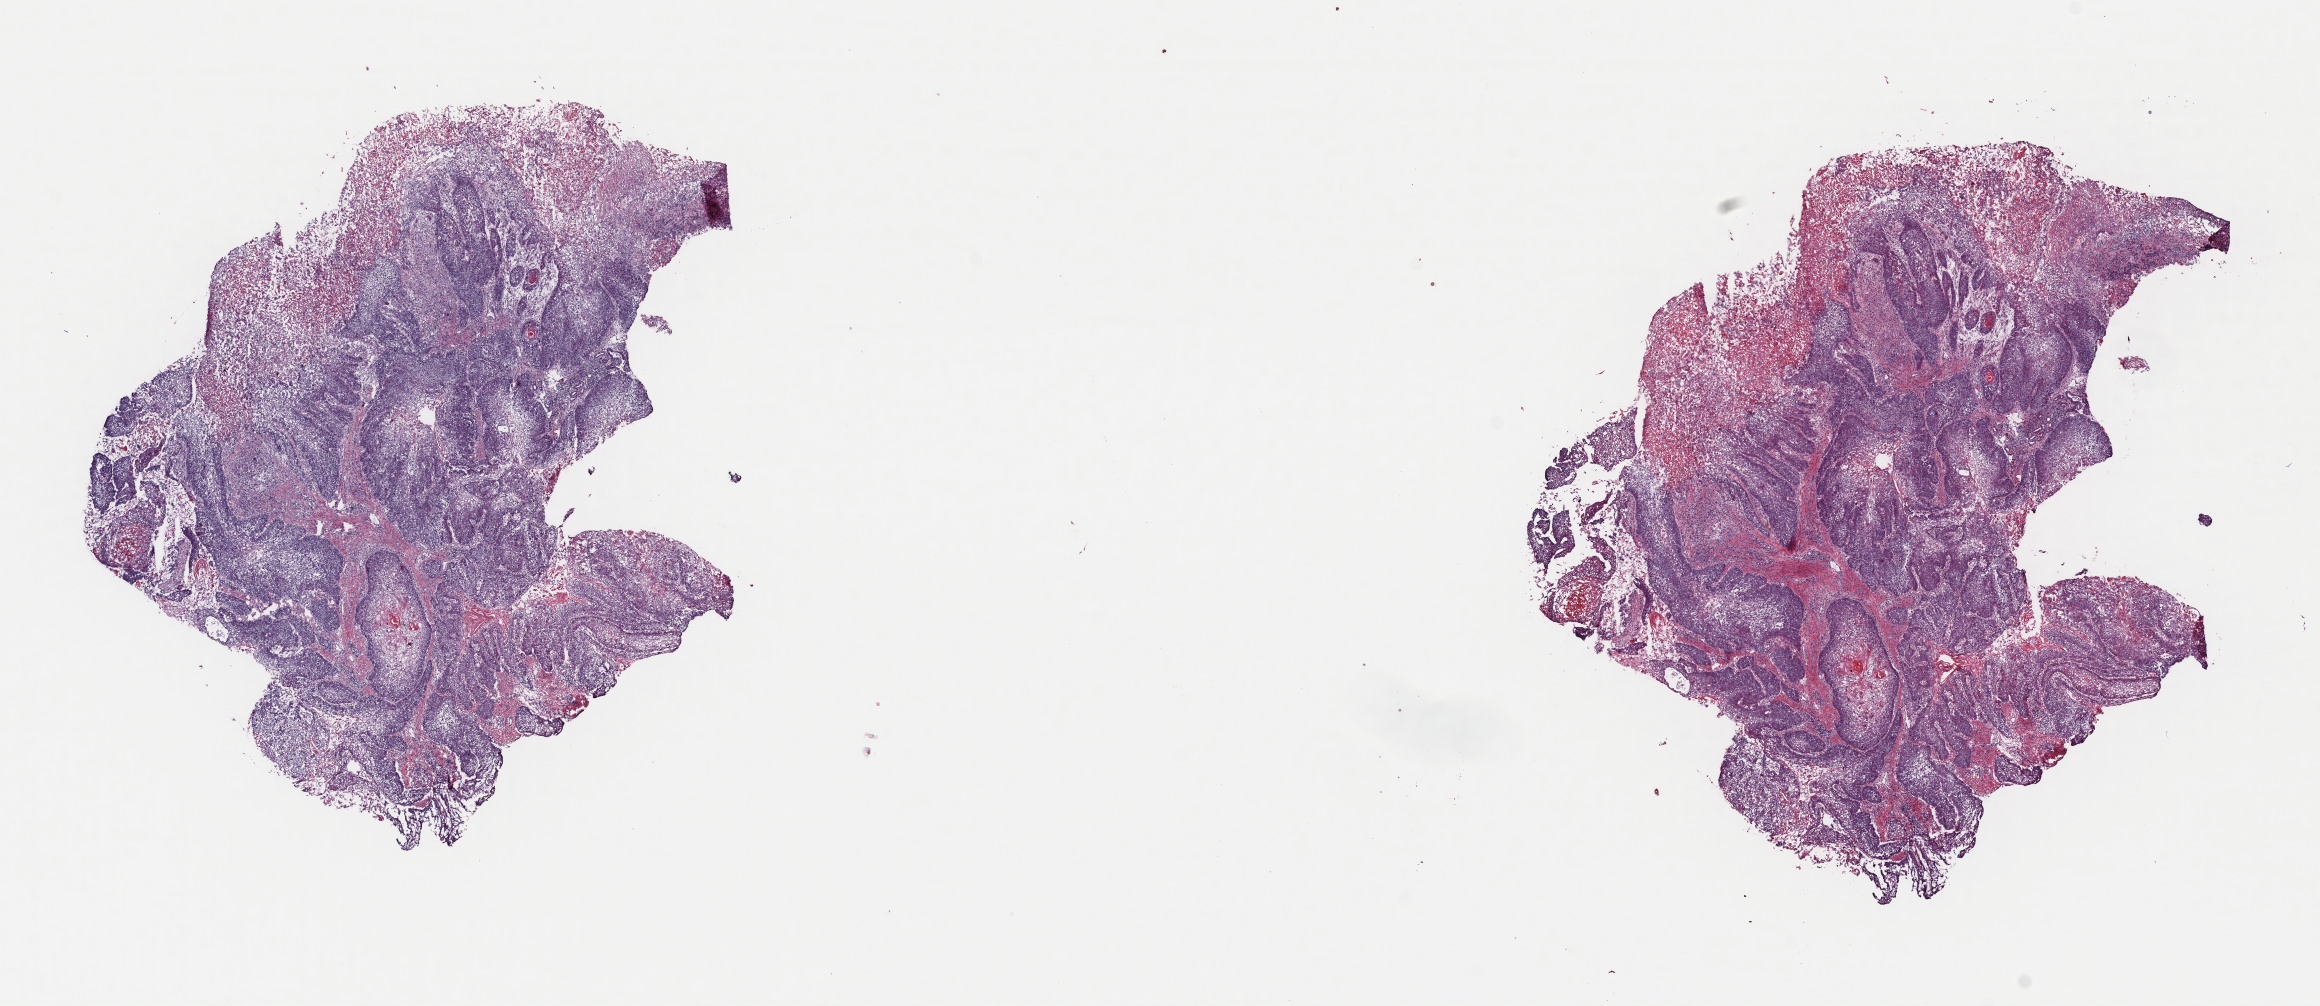
H&E whole-slide image, a low-resolution overview of the entire scanned area, about 18.3 x 7.9 mm; frozen section from the top of the tissue portion; sample: primary tumour, head and neck. Patient: male, age at initial diagnosis 65 years. Histologic grade: G2 (moderately differentiated). Pathologist review of this section (percent, as recorded): tumour cells 70%, tumour nuclei 70%, normal cells 0%, stromal cells 10%, necrosis 20%. Inflammatory infiltration, as recorded: lymphocyte infiltration 40%, monocyte infiltration 20%, neutrophil infiltration 20%.
AJCC pathologic stage: II (7th edition). Histologic diagnosis: Squamous cell carcinoma, keratinizing, NOS (larynx, NOS).